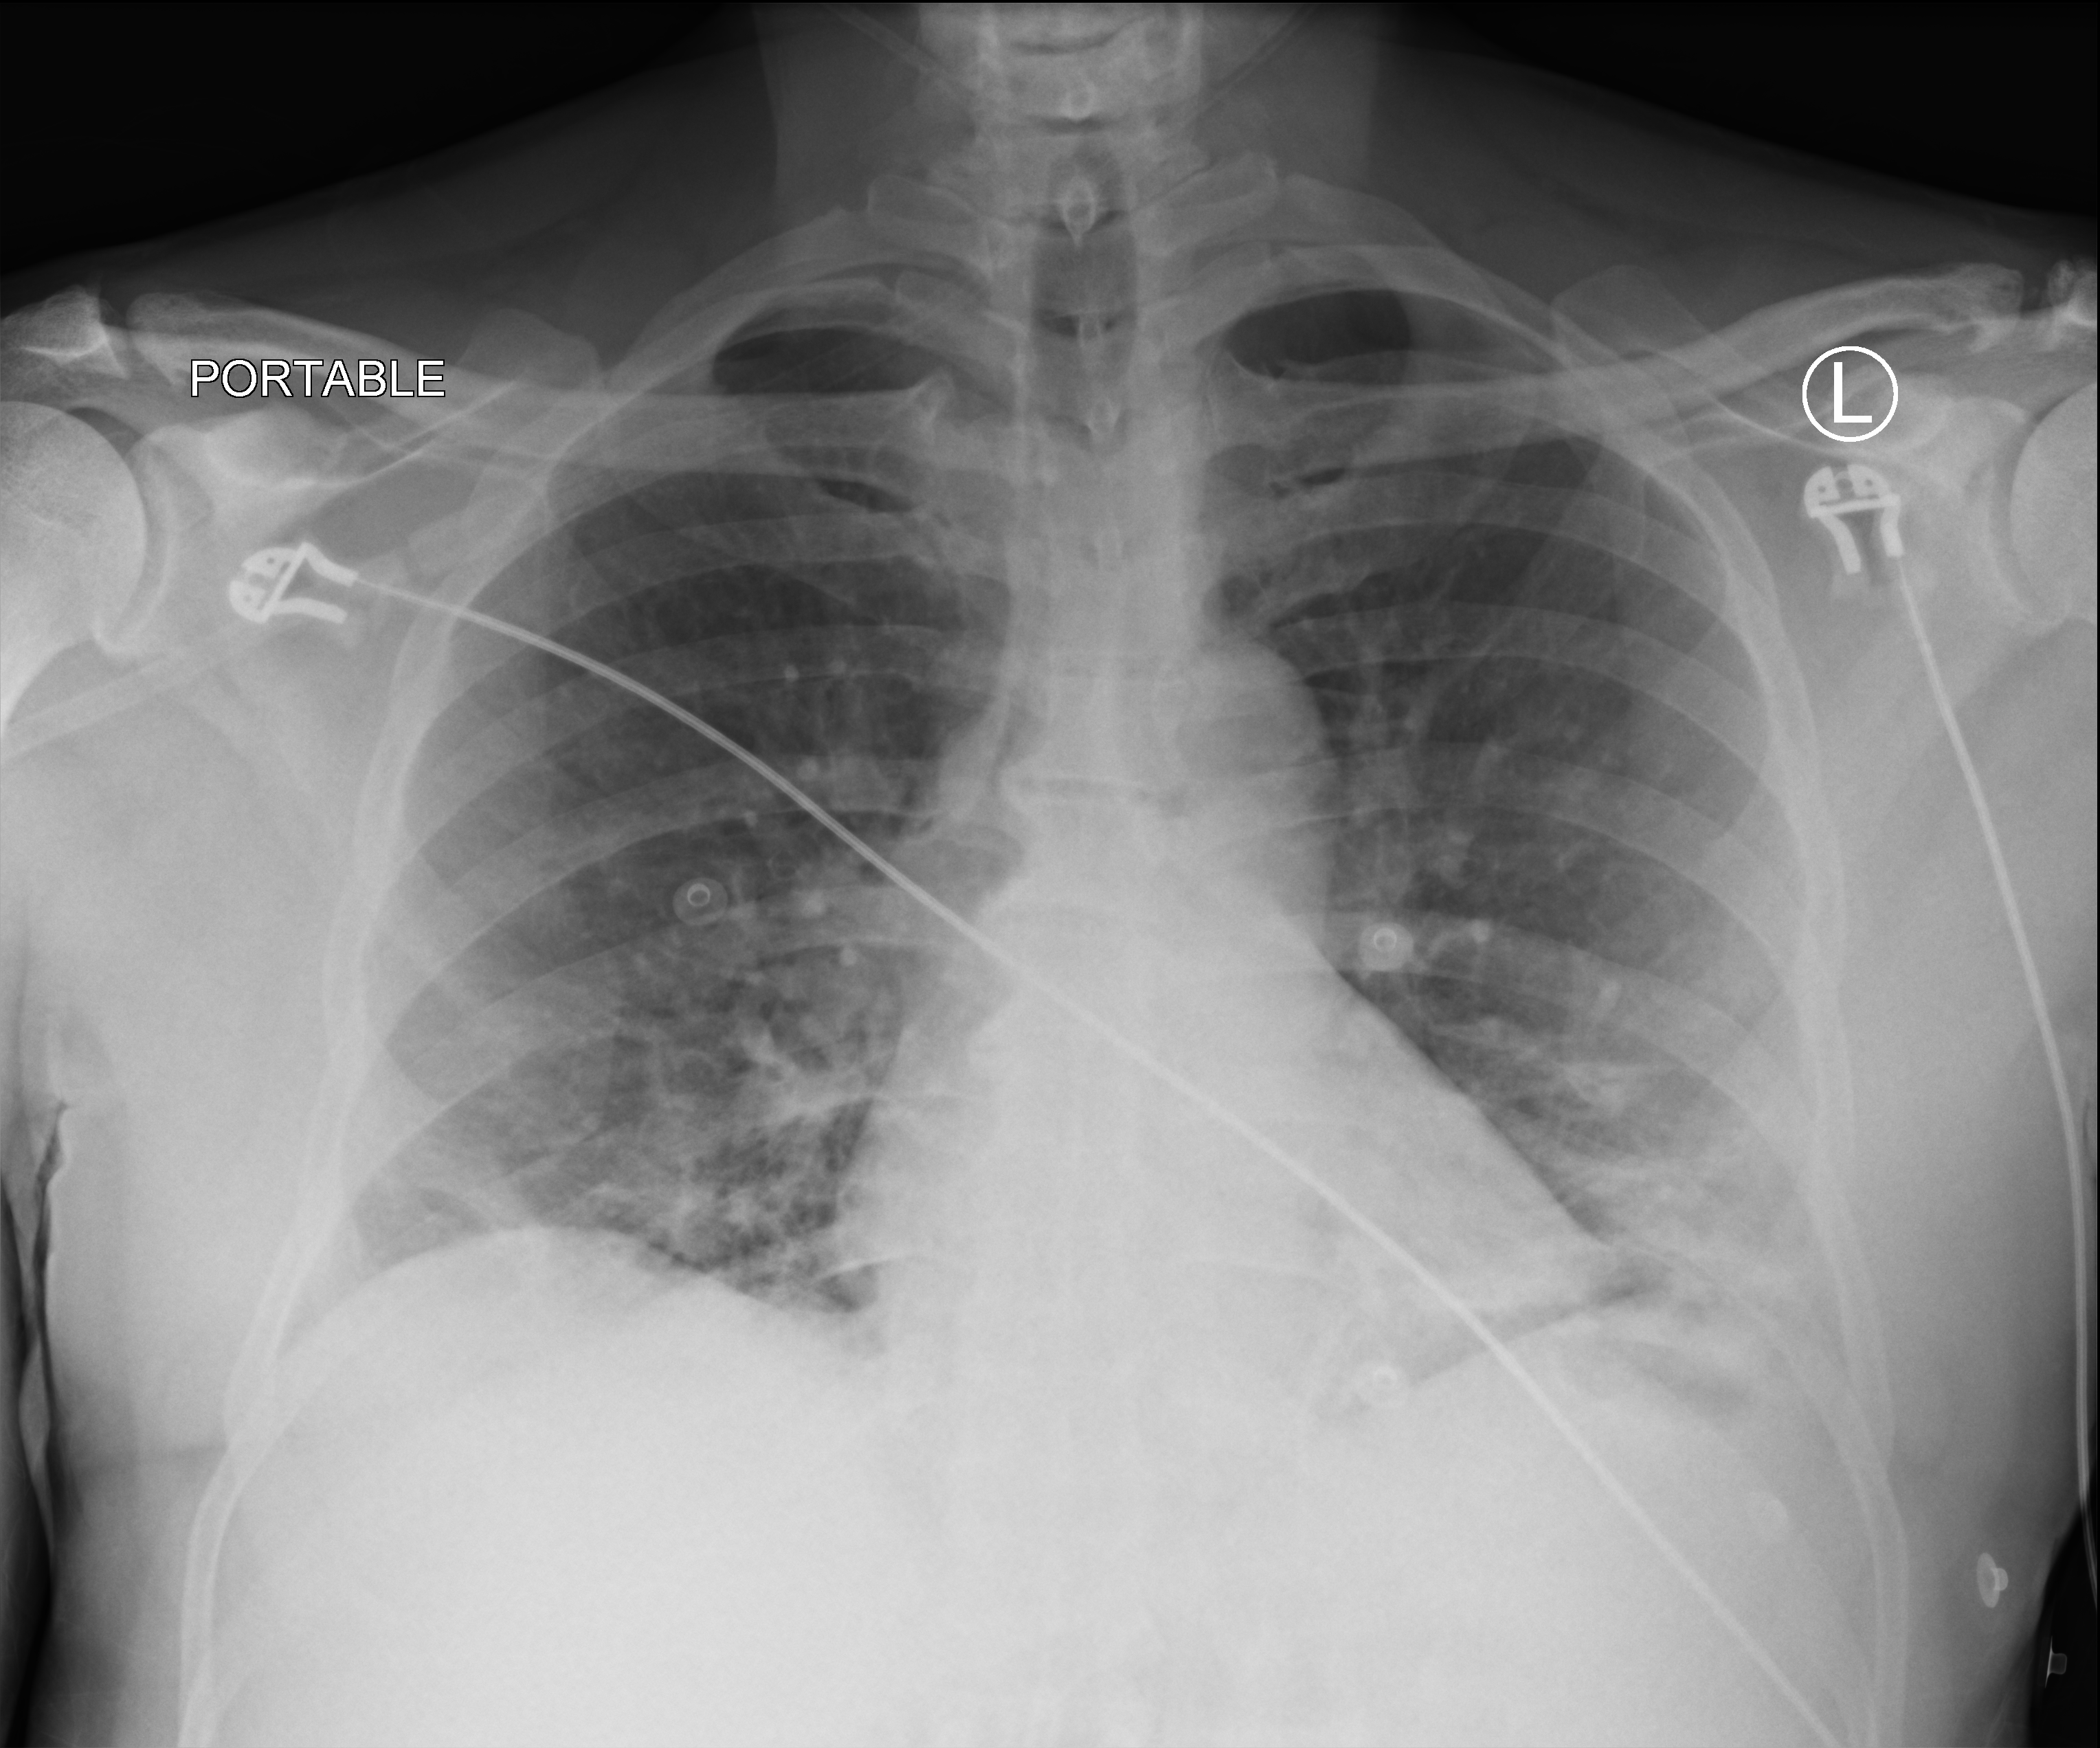
Bedside chest radiograph (computed radiography), anteroposterior (AP) projection. Patient hospitalised with COVID-19; male, aged 18–59 years.
Hospital-stay facts (about this admission, not read from this image; timing relative to this image not recorded):
- mechanically ventilated during this hospital stay: no